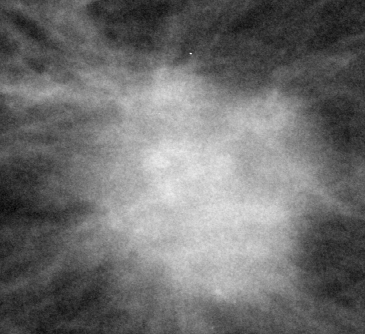
Region of interest cut from a scanned film mammogram (one marked finding), right breast, MLO view.
Finding: mass, shape irregular, margins spiculated; BI-RADS assessment category 5; pathology (as recorded): malignant.